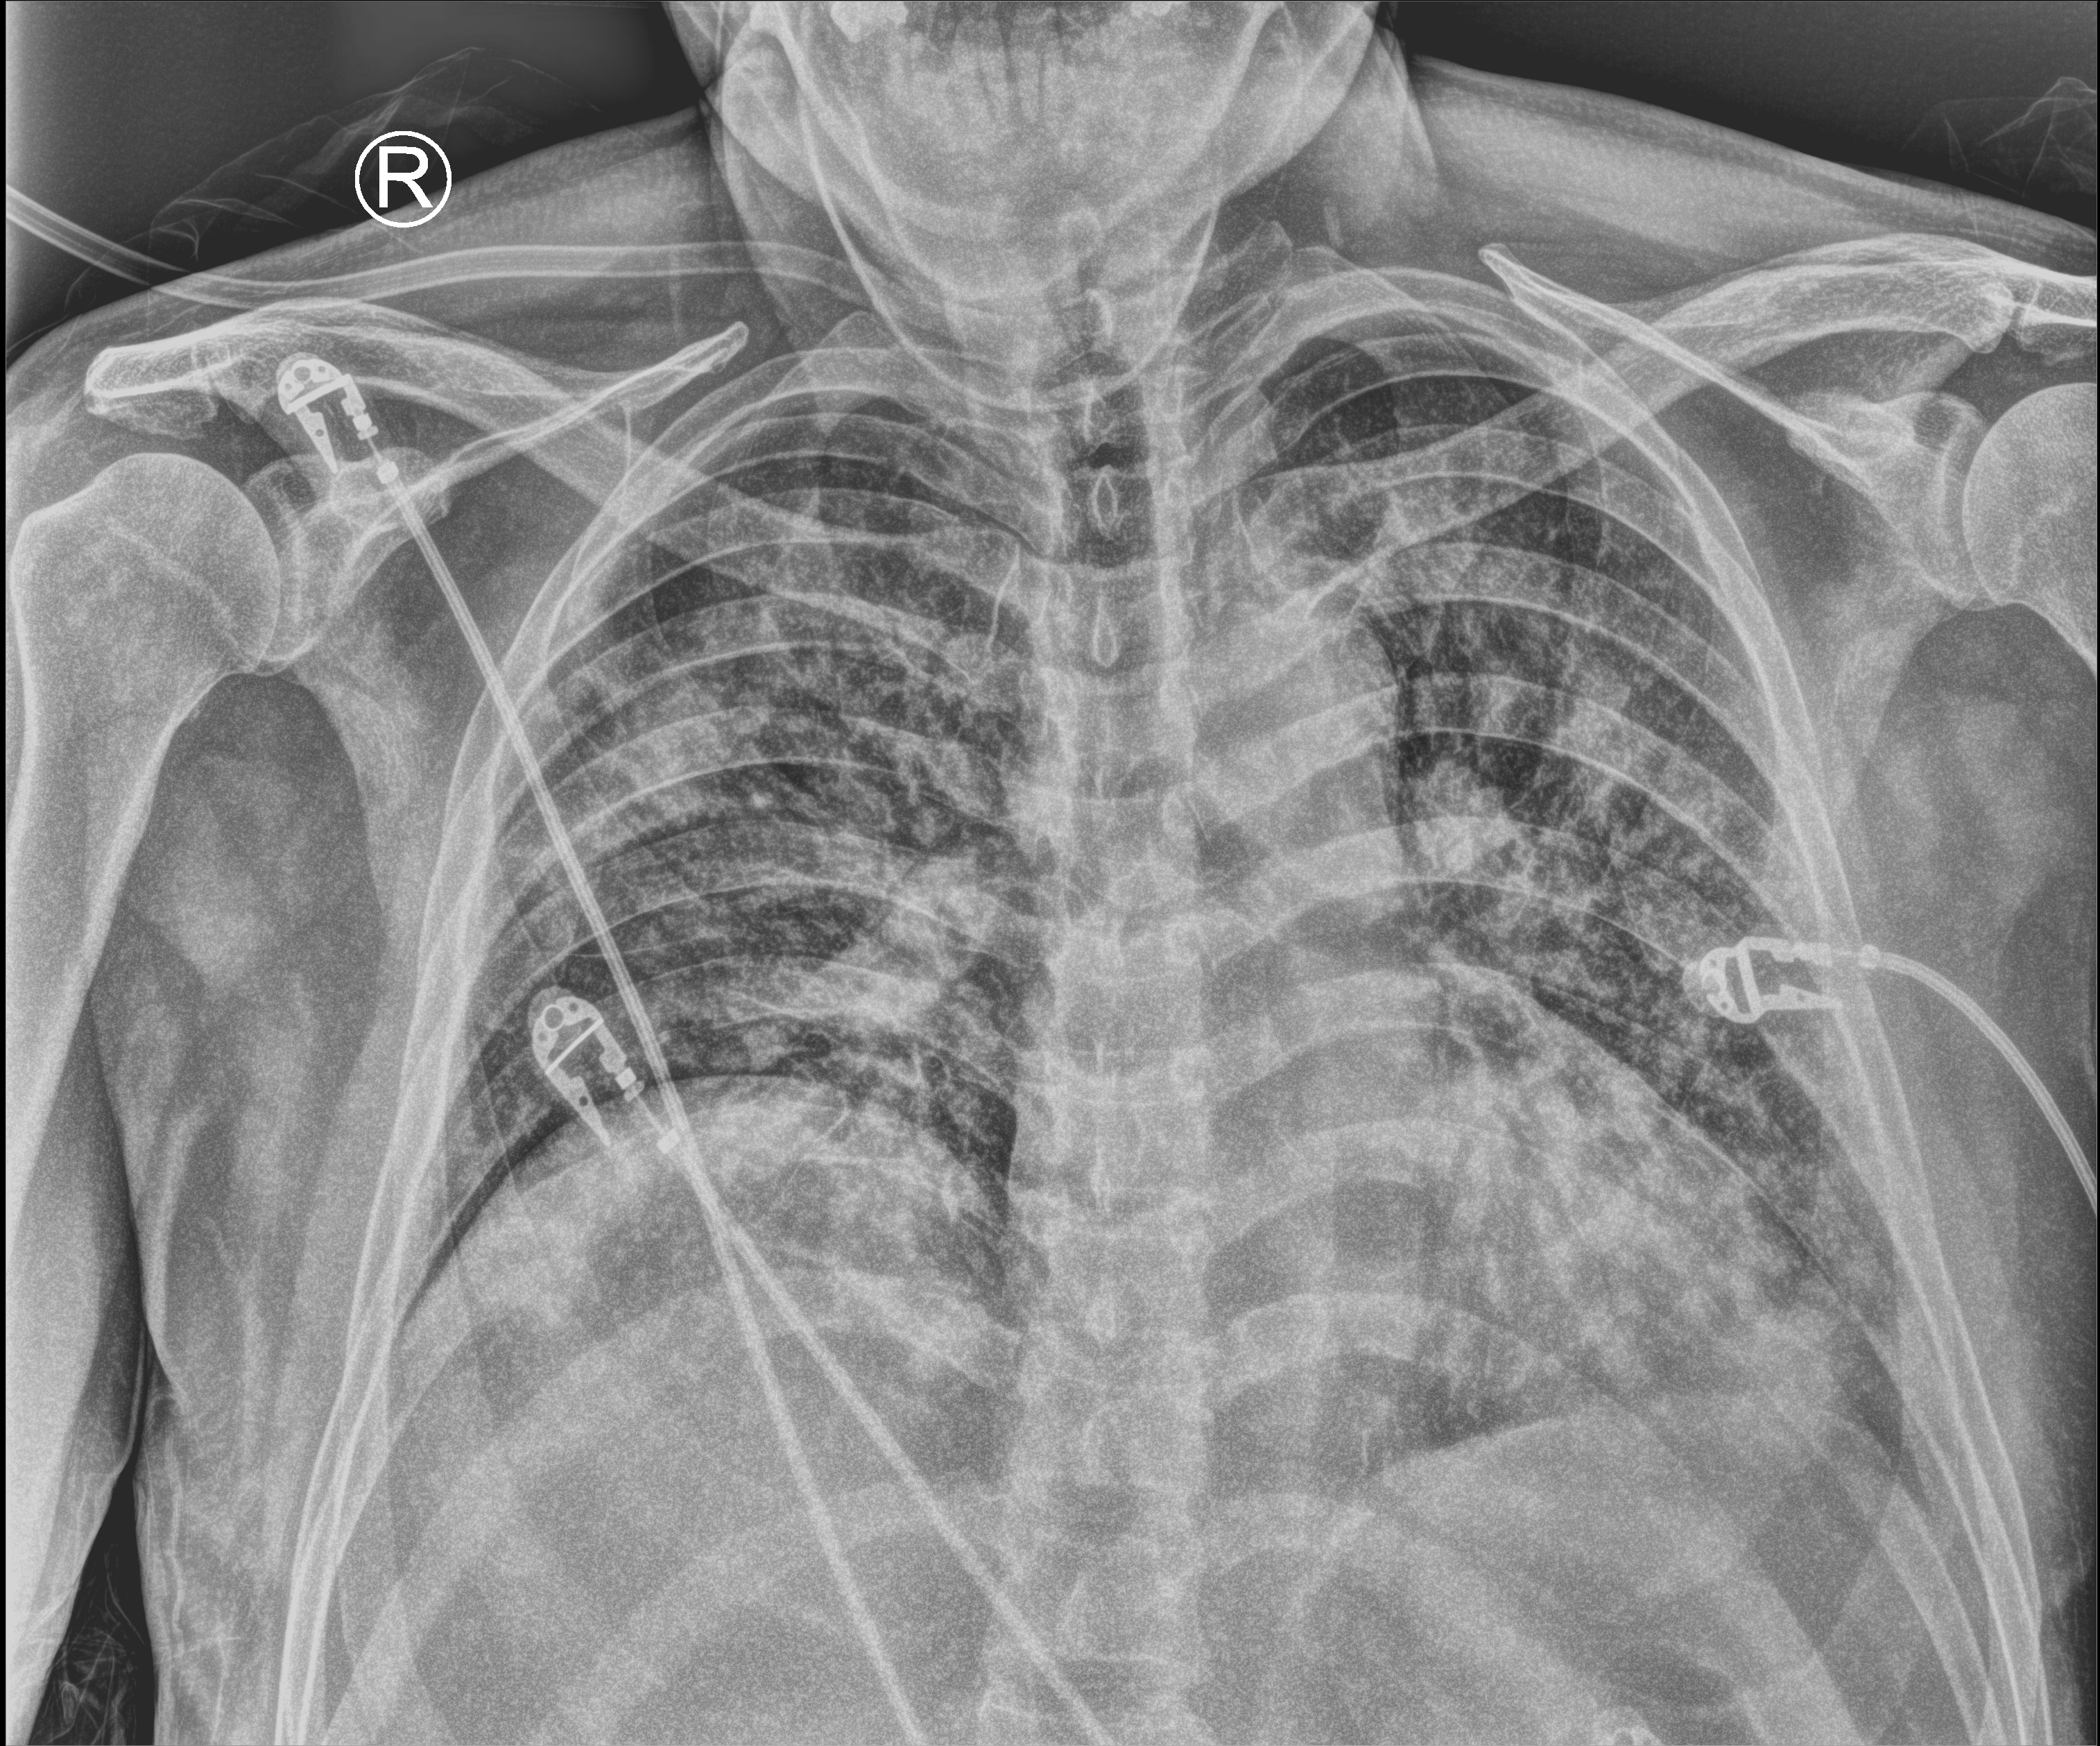
Chest X-ray (portable), anteroposterior (AP) projection. Male patient hospitalised with COVID-19, age 60–74 years.
From the hospital-stay record, not from the radiograph (when in the stay this image was taken is not recorded): mechanically ventilated during this hospital stay: no; diabetes (admission record): no.